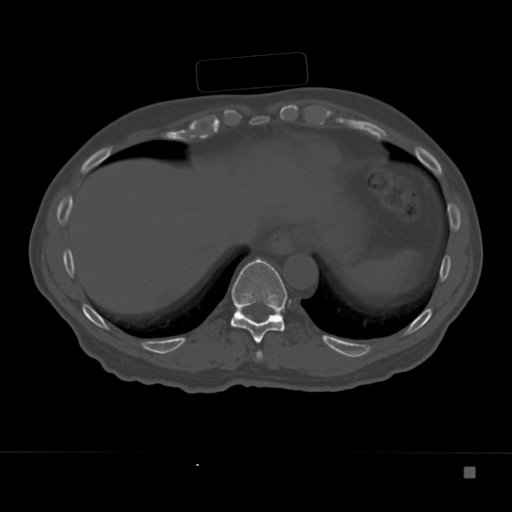
CT including the spine, one axial slice. Reconstruction kernel Br40s. Bone window (W 1800 / L 400 HU). 1.5 mm slice thickness. 512 × 512 image matrix, field of view 389 × 389 mm. Male patient, age 72 years. Case-level facts recorded for this patient, not image findings: primary cancer: skeletal.
Annotated regions visible in this slice (semi-automatically segmented with operator editing):
- T10 vertebra: bounding box (x1, y1, x2, y2) in pixels: (230, 258, 288, 344)
- T9 vertebra: (256, 351, 263, 360)